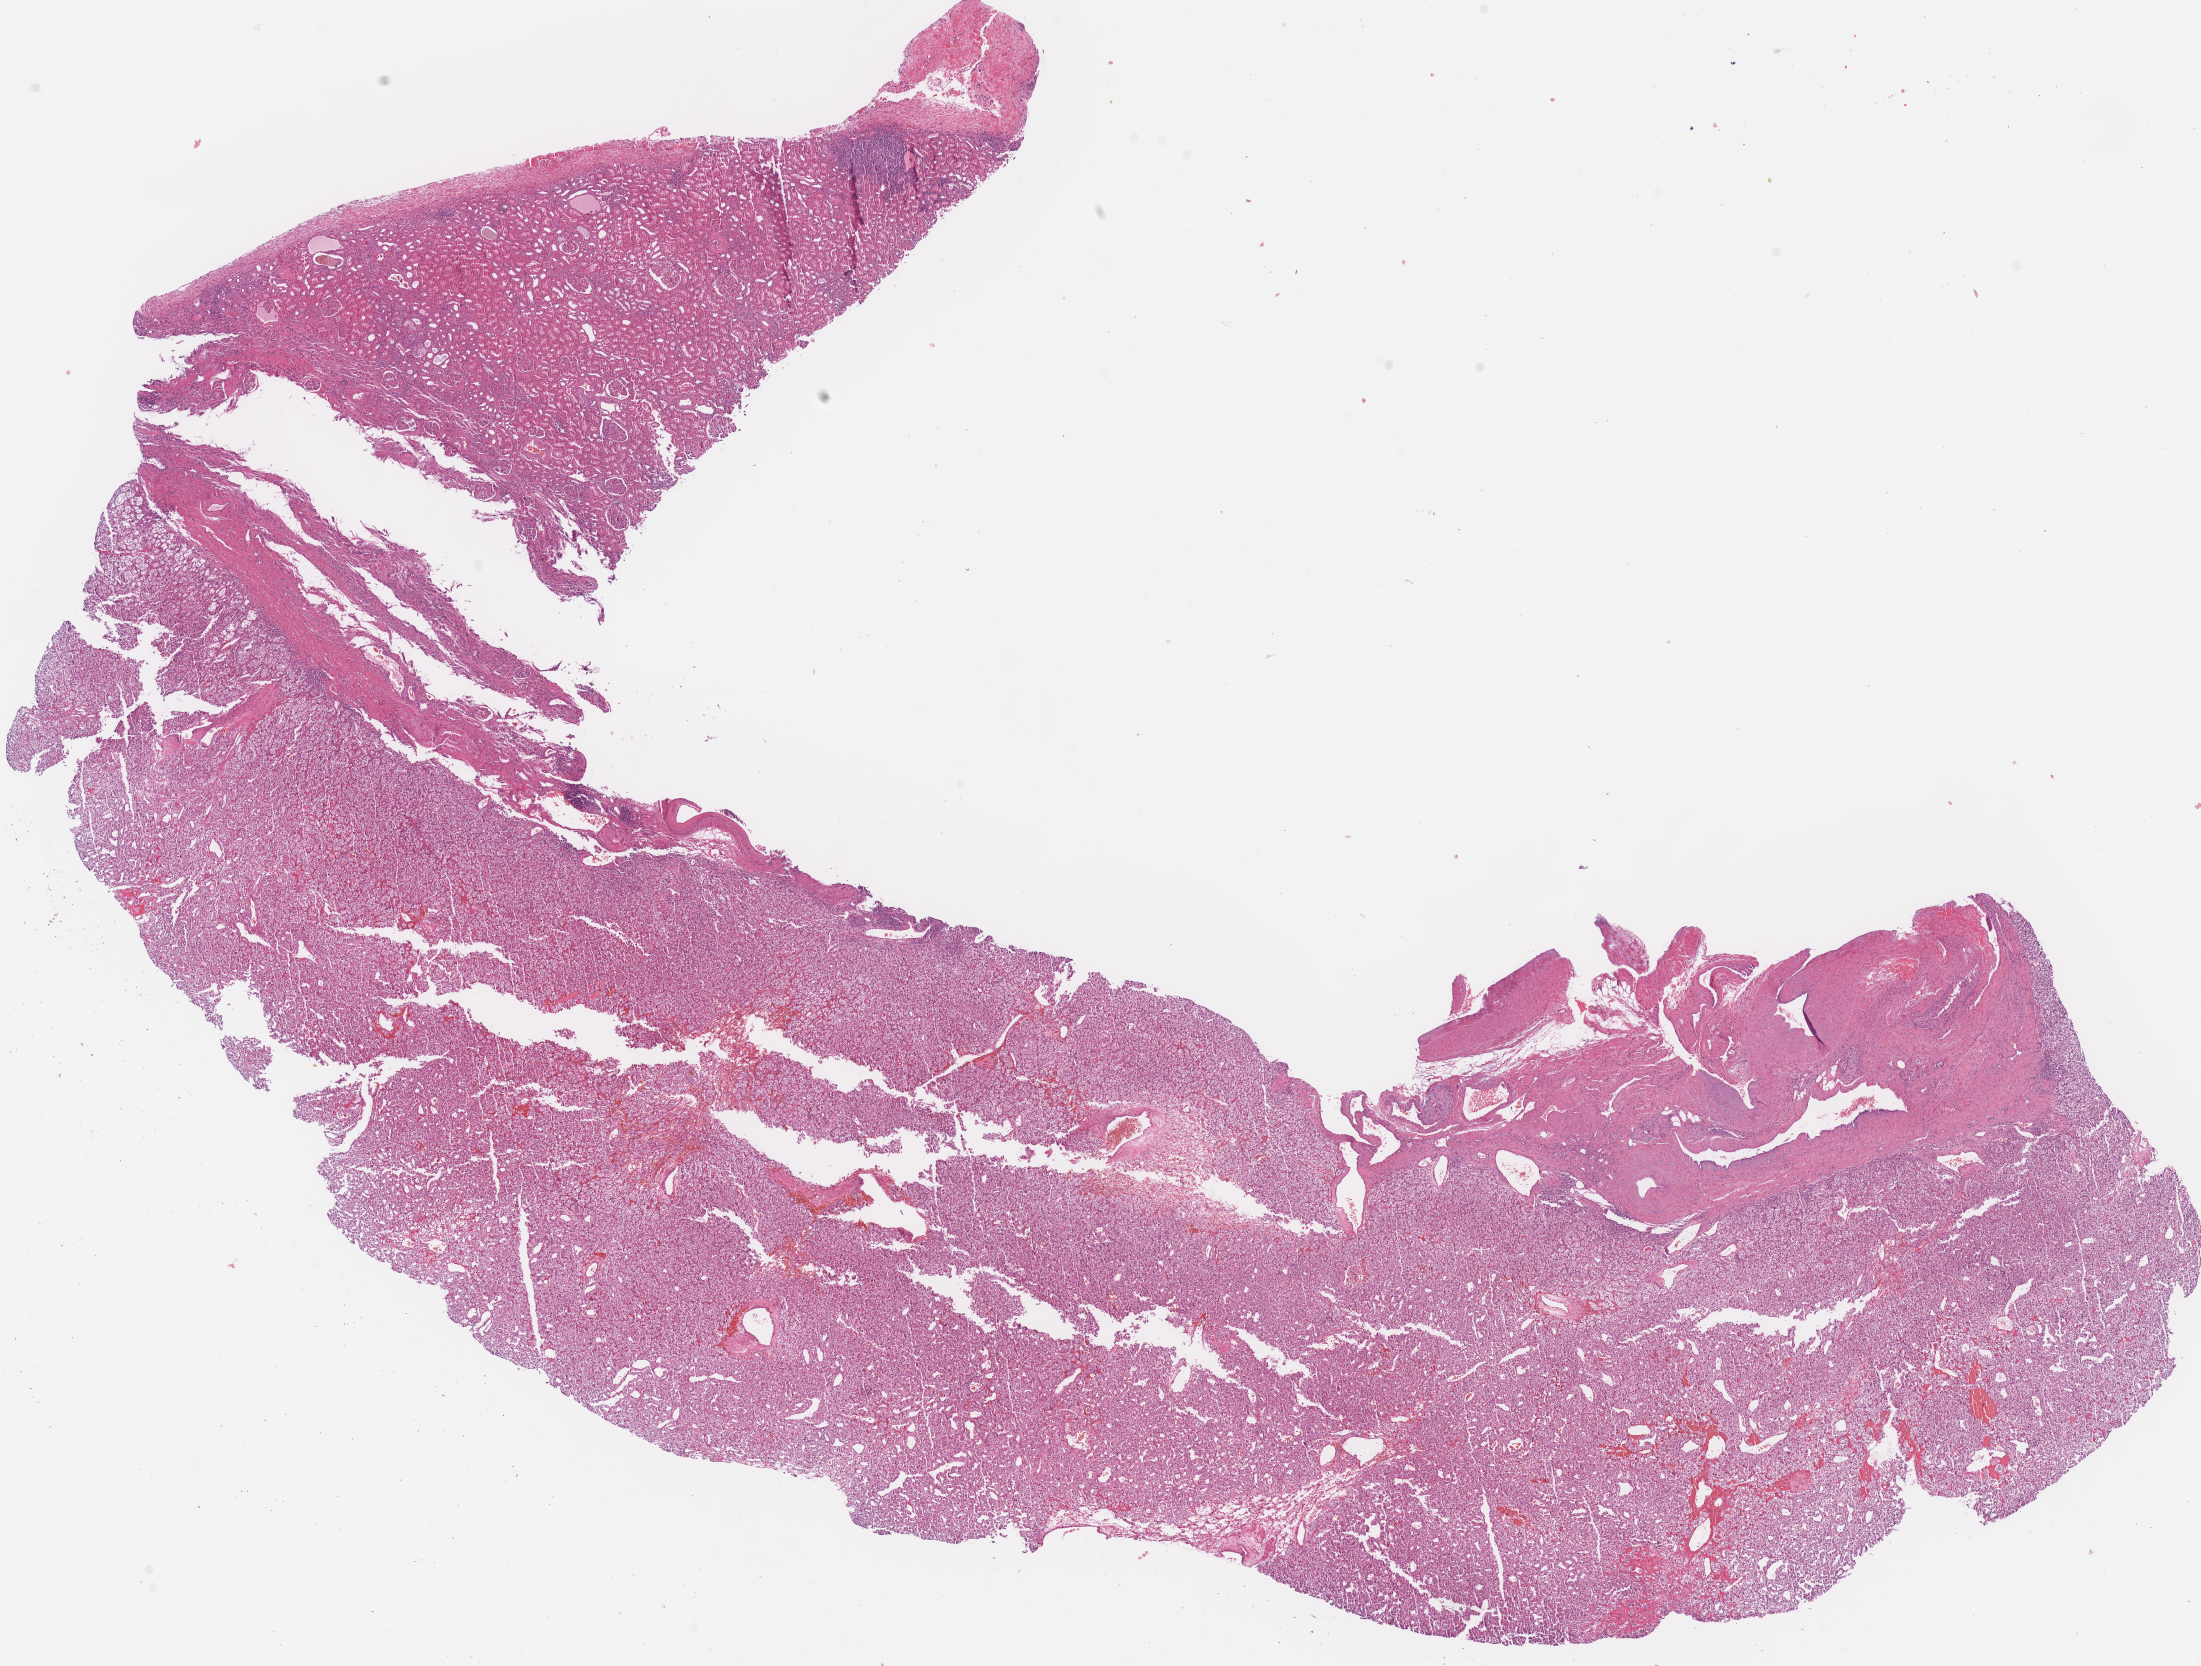
Whole-slide histology image, H&E — whole scanned area (about 17.3 x 13.1 mm, slide scanned at 40x) shown as a low-resolution overview. Formalin-fixed paraffin-embedded (FFPE) diagnostic section. Sample: primary tumour, kidney. Female, age 82 years at initial diagnosis.
Diagnosis: Clear cell adenocarcinoma, NOS.